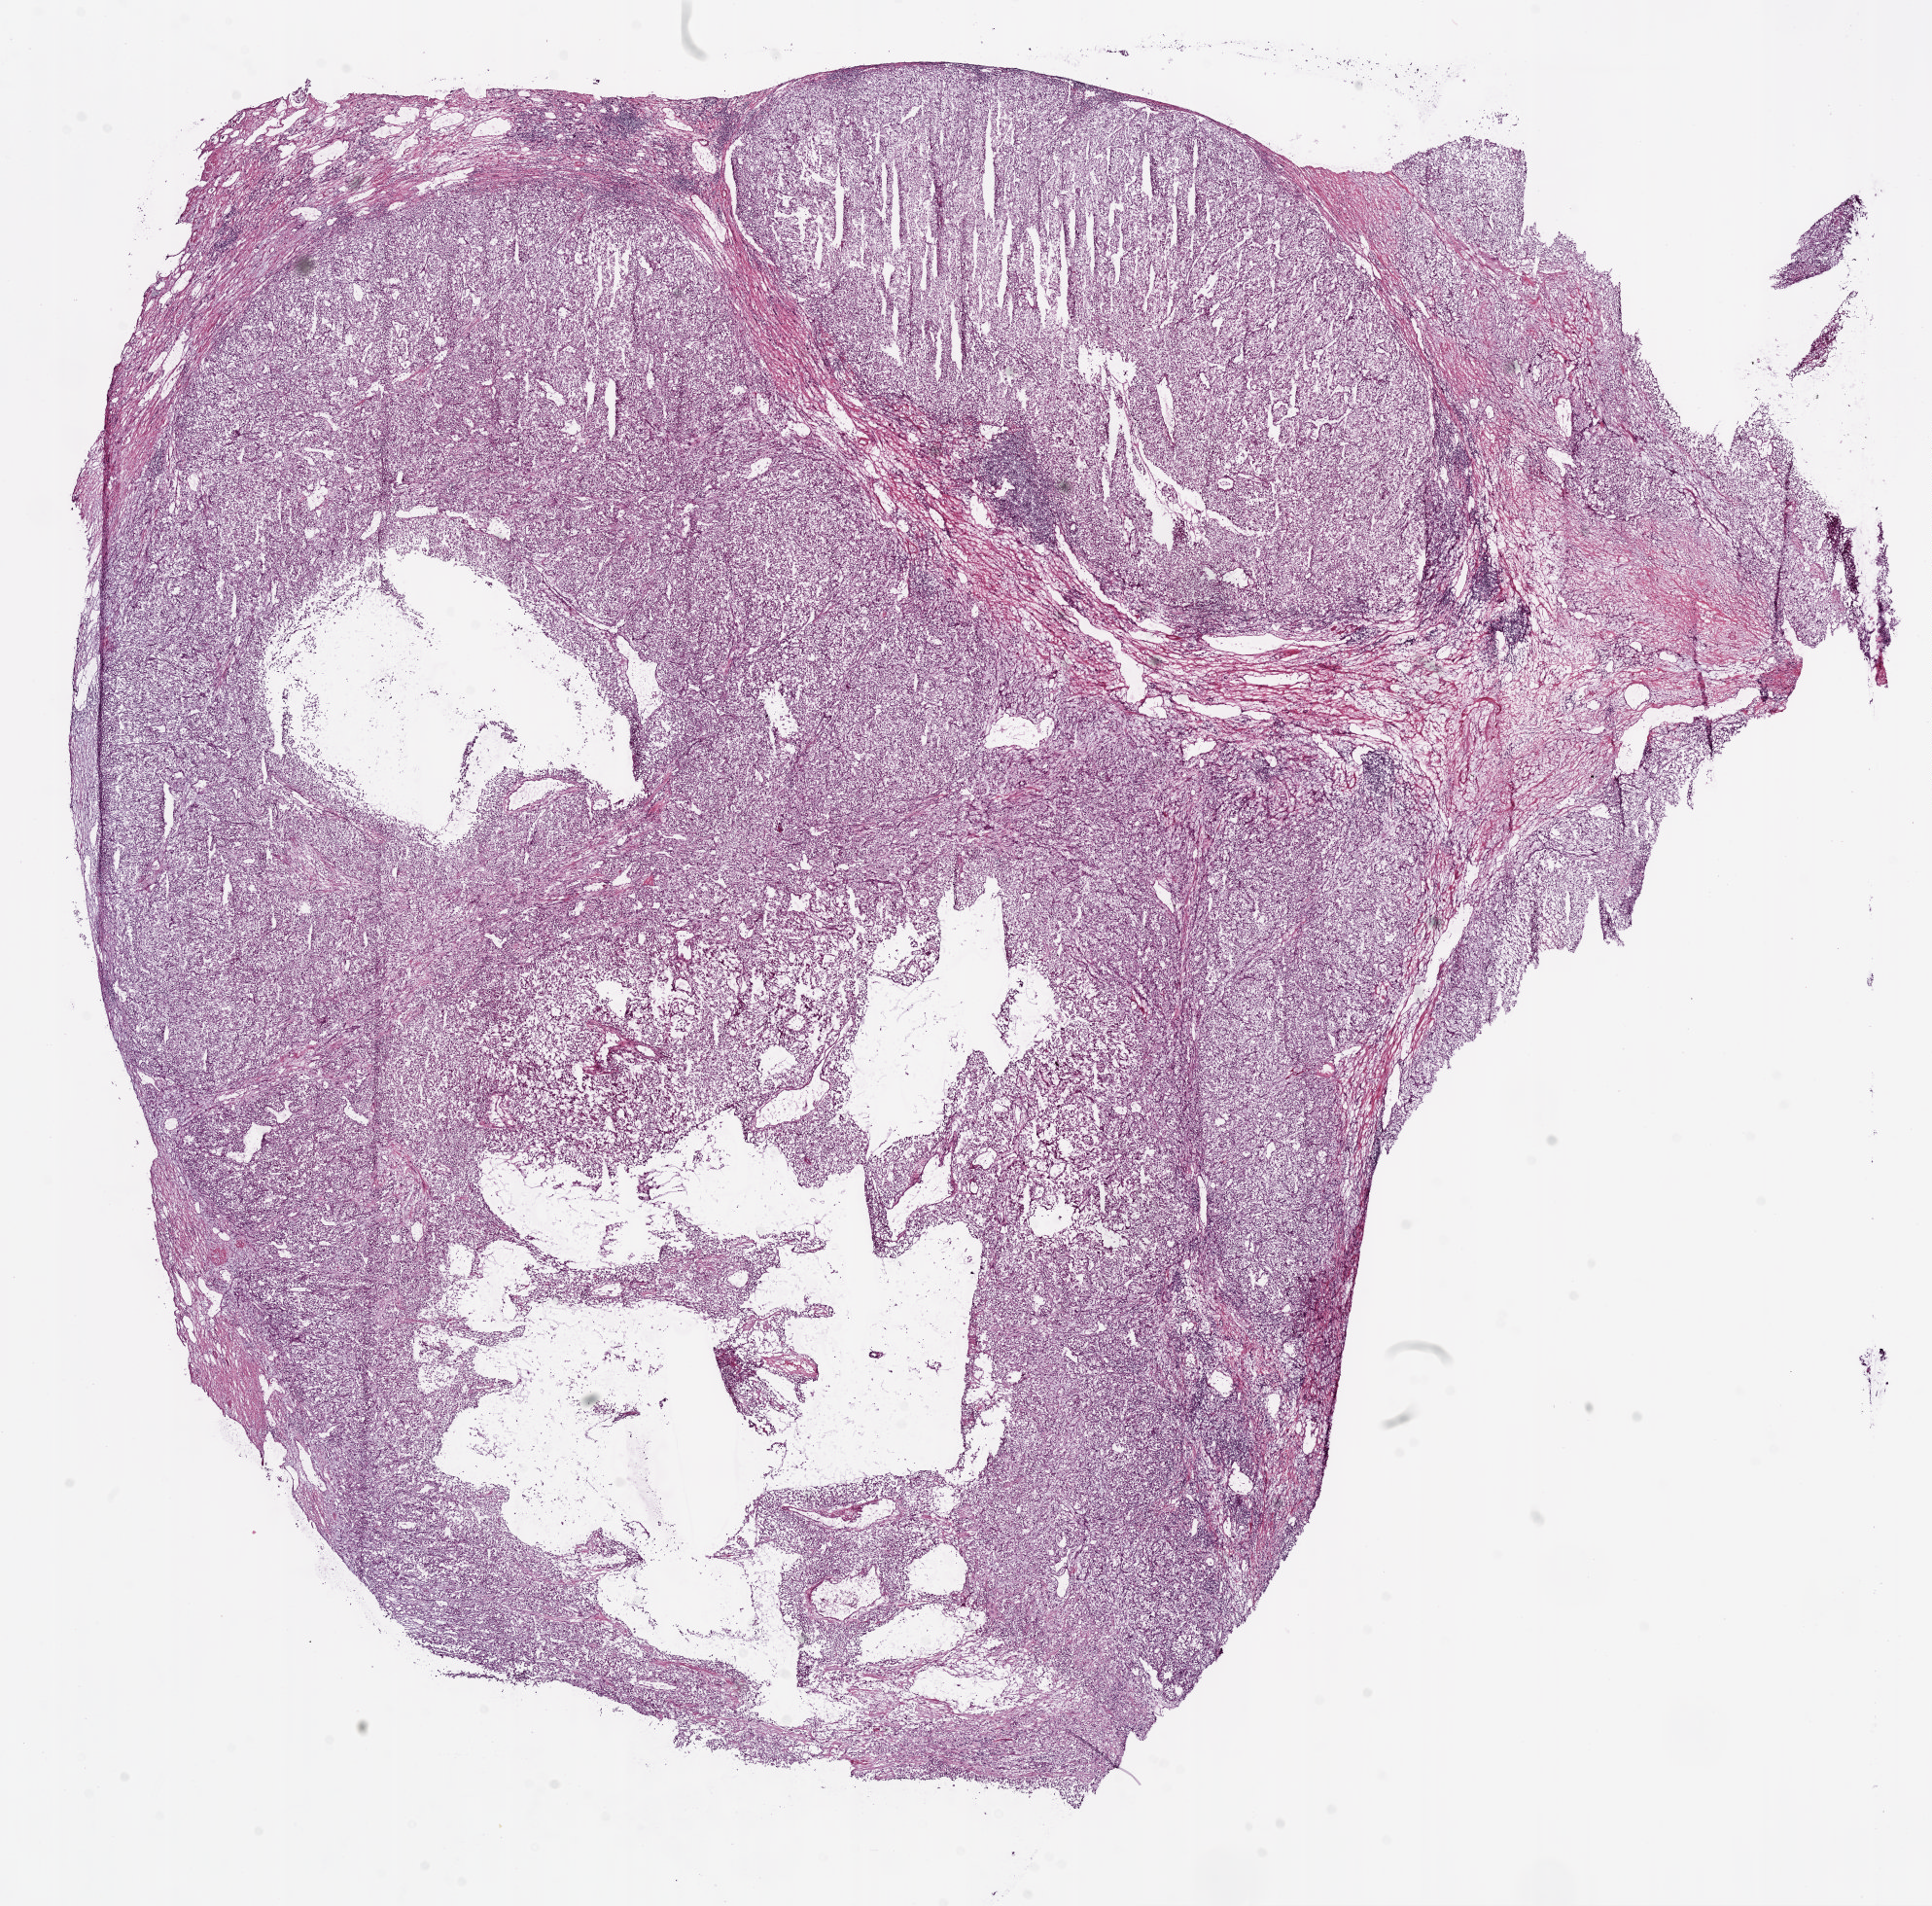
Digitized Hematoxylin and eosin (H&E) stained tissue section (whole slide) — a low-resolution overview of the entire scanned area, about 15.9 x 15.7 mm (from a 5x scan). Frozen section from the top of the tissue portion. Kidney, primary tumour sample. Male patient; age at initial diagnosis 55 years. Histologic grade: G3 (poorly differentiated). Slide review estimates, as recorded: tumour cells 85%, tumour nuclei 75%, normal cells 0%, stromal cells 15%, necrosis 0%.
• AJCC pathologic stage: IV
• laterality: left
• diagnosis: Clear cell adenocarcinoma, NOS